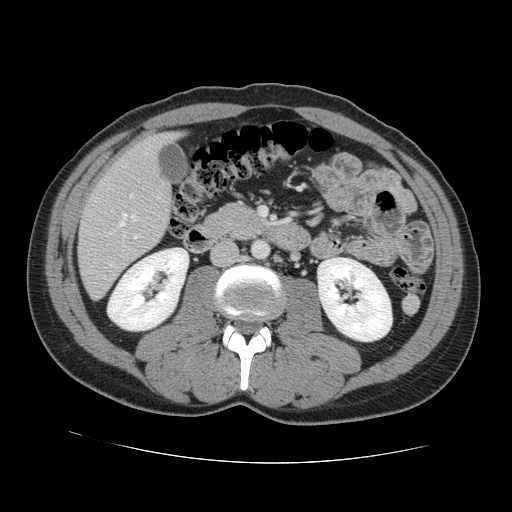
Contrast-enhanced abdominal CT, one axial slice; position 44 of 131 along the scan axis; 120 kVp; intravenous contrast given; soft-tissue window (W 400 / L 40 HU); 2.5 mm slice thickness; 512 × 512 image matrix. Male patient, age 40 years. Case-level facts recorded for this patient, not image findings: diagnosis: colorectal cancer liver metastases, imaged before liver resection; multiple liver metastases: yes; largest metastasis: 2.9 cm; disease in both lobes: yes.
Outlined on this slice (expert manual segmentation):
- hepatic veins: box from (x=120, y=214) to (x=136, y=226) px
- liver: (x=79, y=135)–(x=175, y=298)
- planned liver remnant (the part of the liver to remain after resection): (x=129, y=135)–(x=172, y=165)
- portal vein (with intrahepatic branches): (x=130, y=194)–(x=138, y=239)